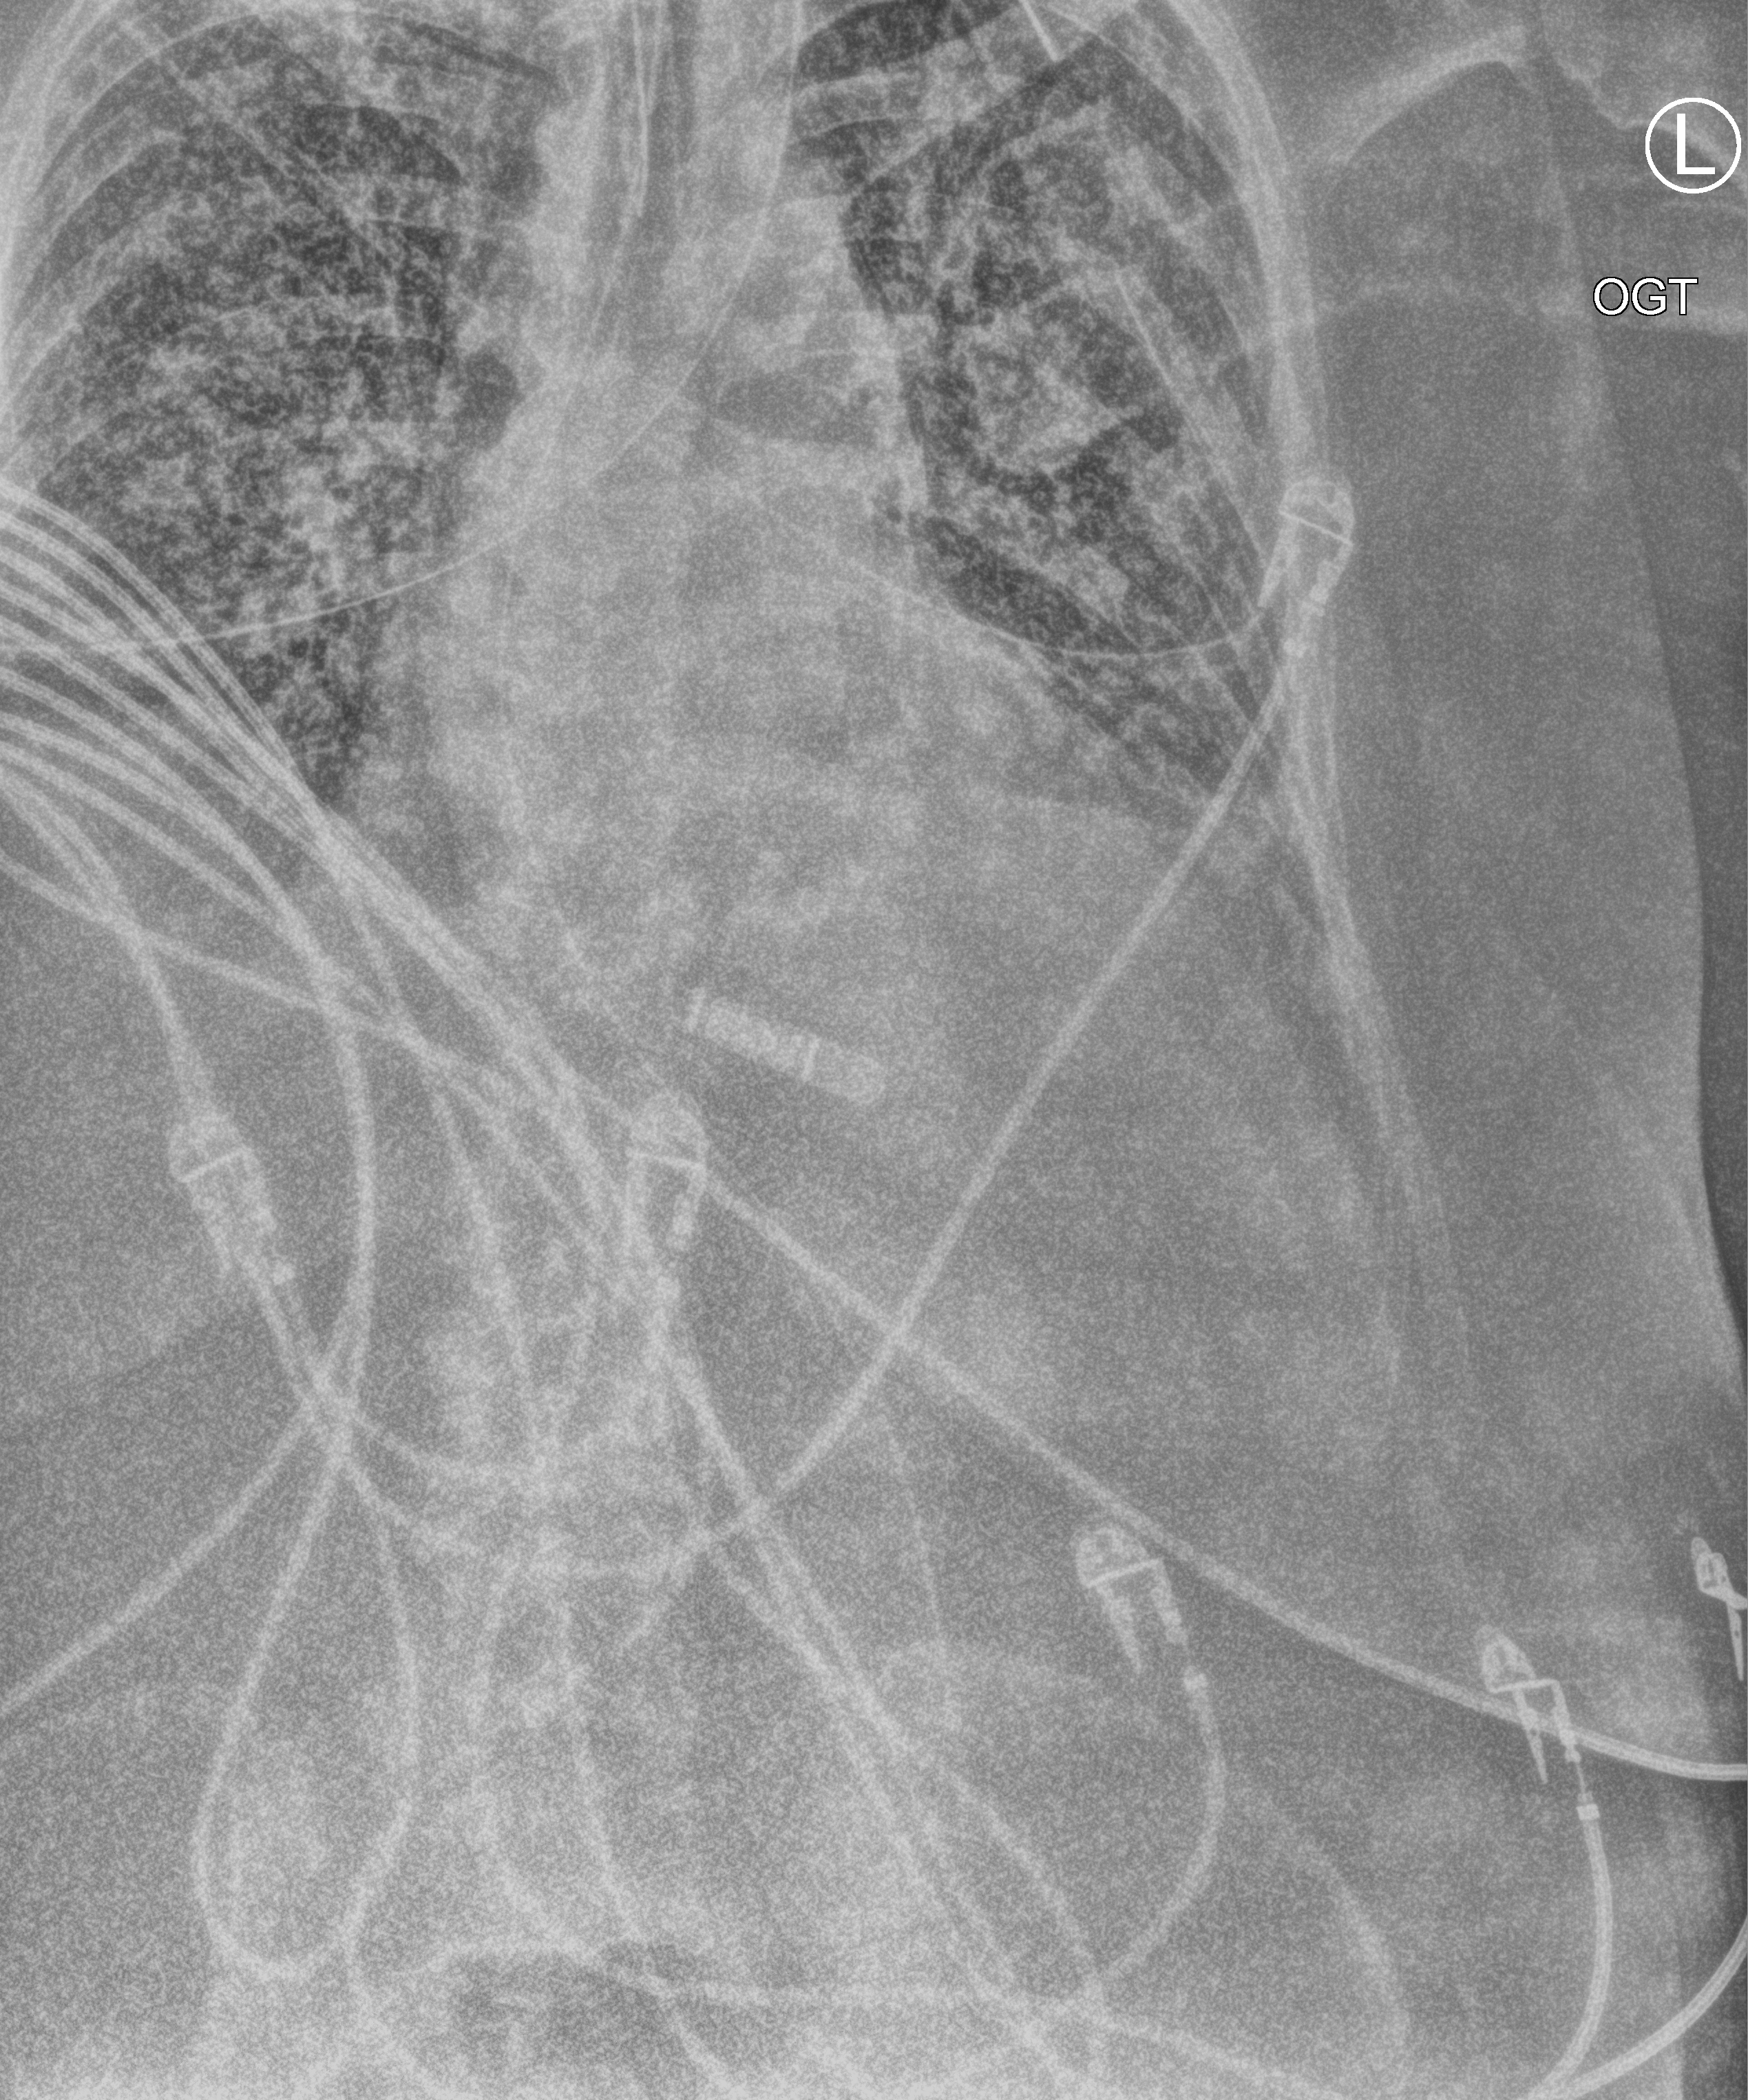
Chest X-ray (portable); anteroposterior (AP) projection. Patient hospitalised with COVID-19; female, aged 60–74 years.
Hospital-stay facts (about this admission, not read from this image; timing relative to this image not recorded): mechanically ventilated during this hospital stay: yes; admitted to intensive care during this hospital stay: yes.